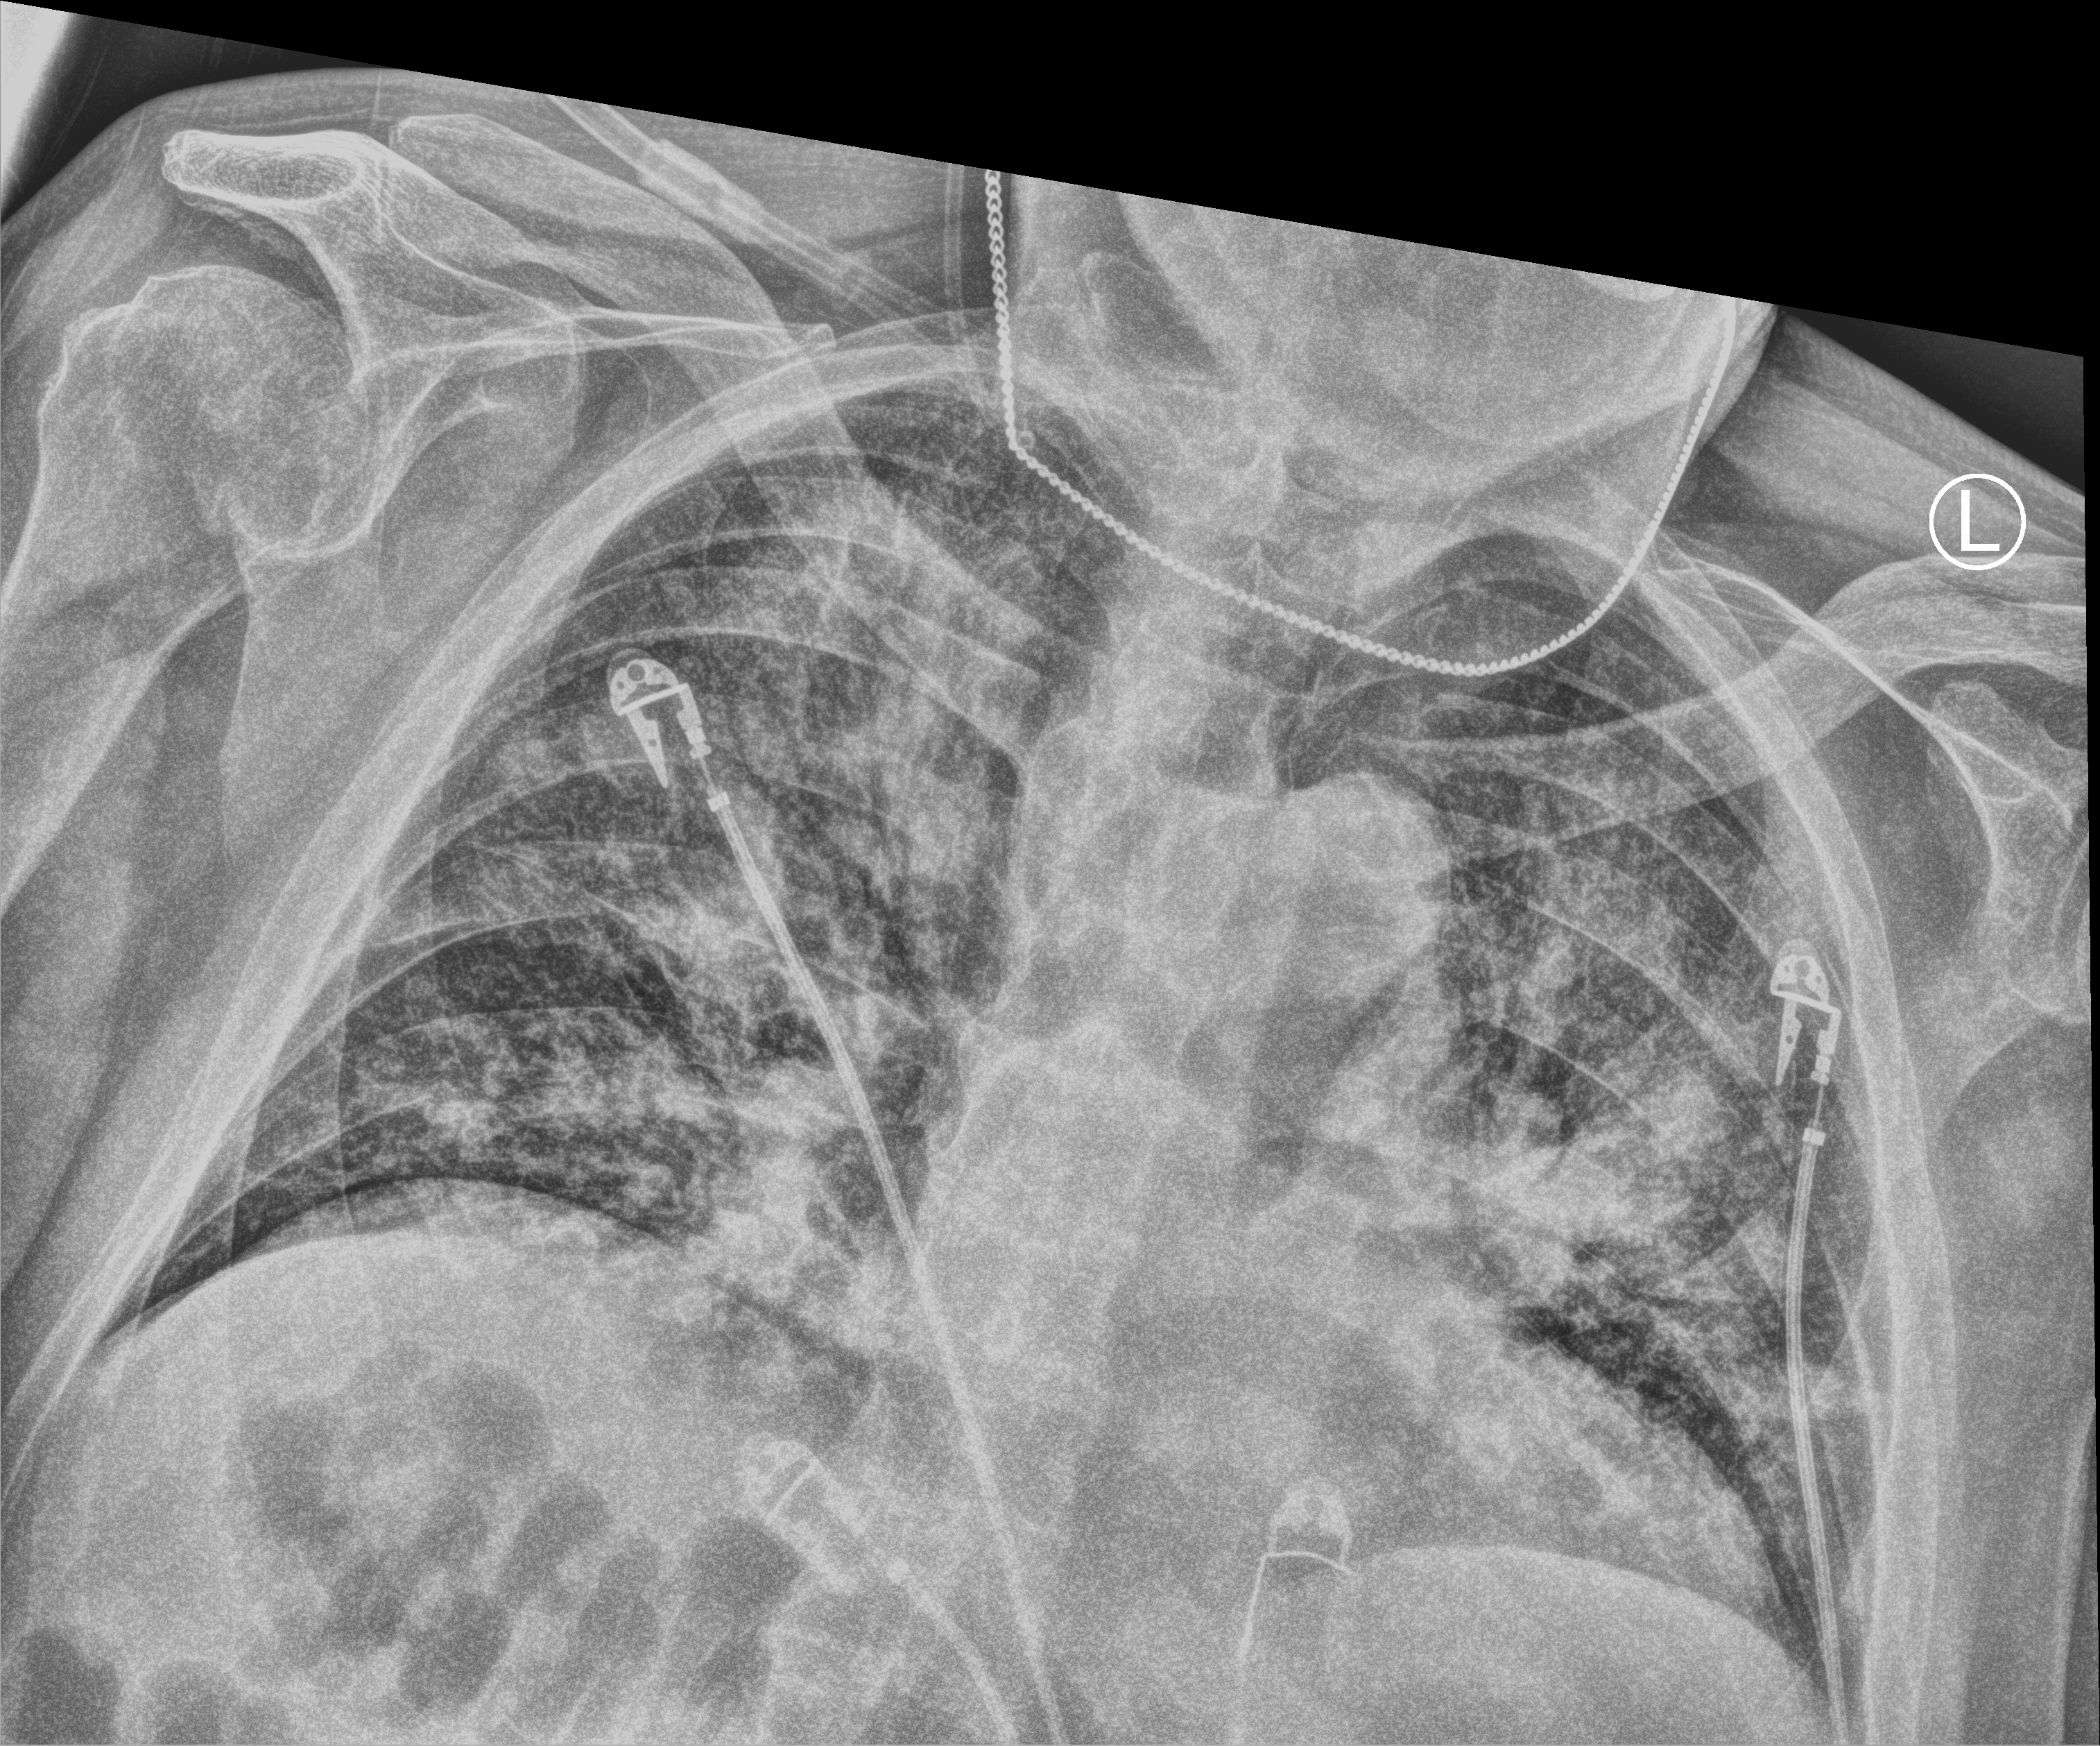
Chest X-ray (portable), anteroposterior (AP) projection. Patient hospitalised with COVID-19; male, aged 75–90 years.
Hospital-stay facts (about this admission, not read from this image; timing relative to this image not recorded):
- diabetes (admission record): no
- smoking status (admission record): never